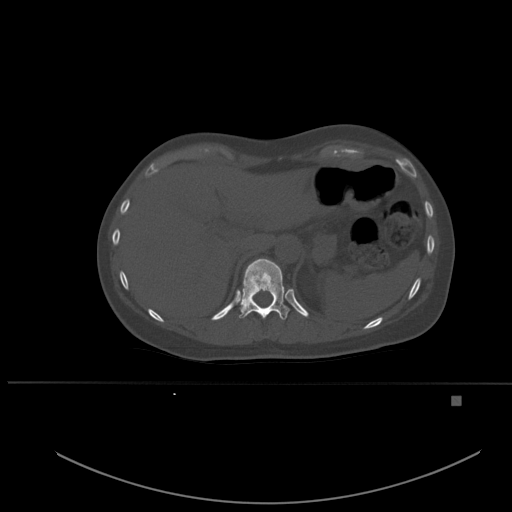
CT including the spine, one axial slice. Position 273 of 651 along the scan axis. Bone window (W 1800 / L 400 HU). 512 × 512 image matrix. Patient: female, 49 years. From the clinical record (not read from this slice): primary cancer: breast; vertebrae with lytic lesions (as recorded): L3, T12, L4.
Structures marked on this image (semi-automatic segmentation, software-assisted and operator-edited):
- T11 vertebra: box from (x=239, y=259) to (x=290, y=320) px